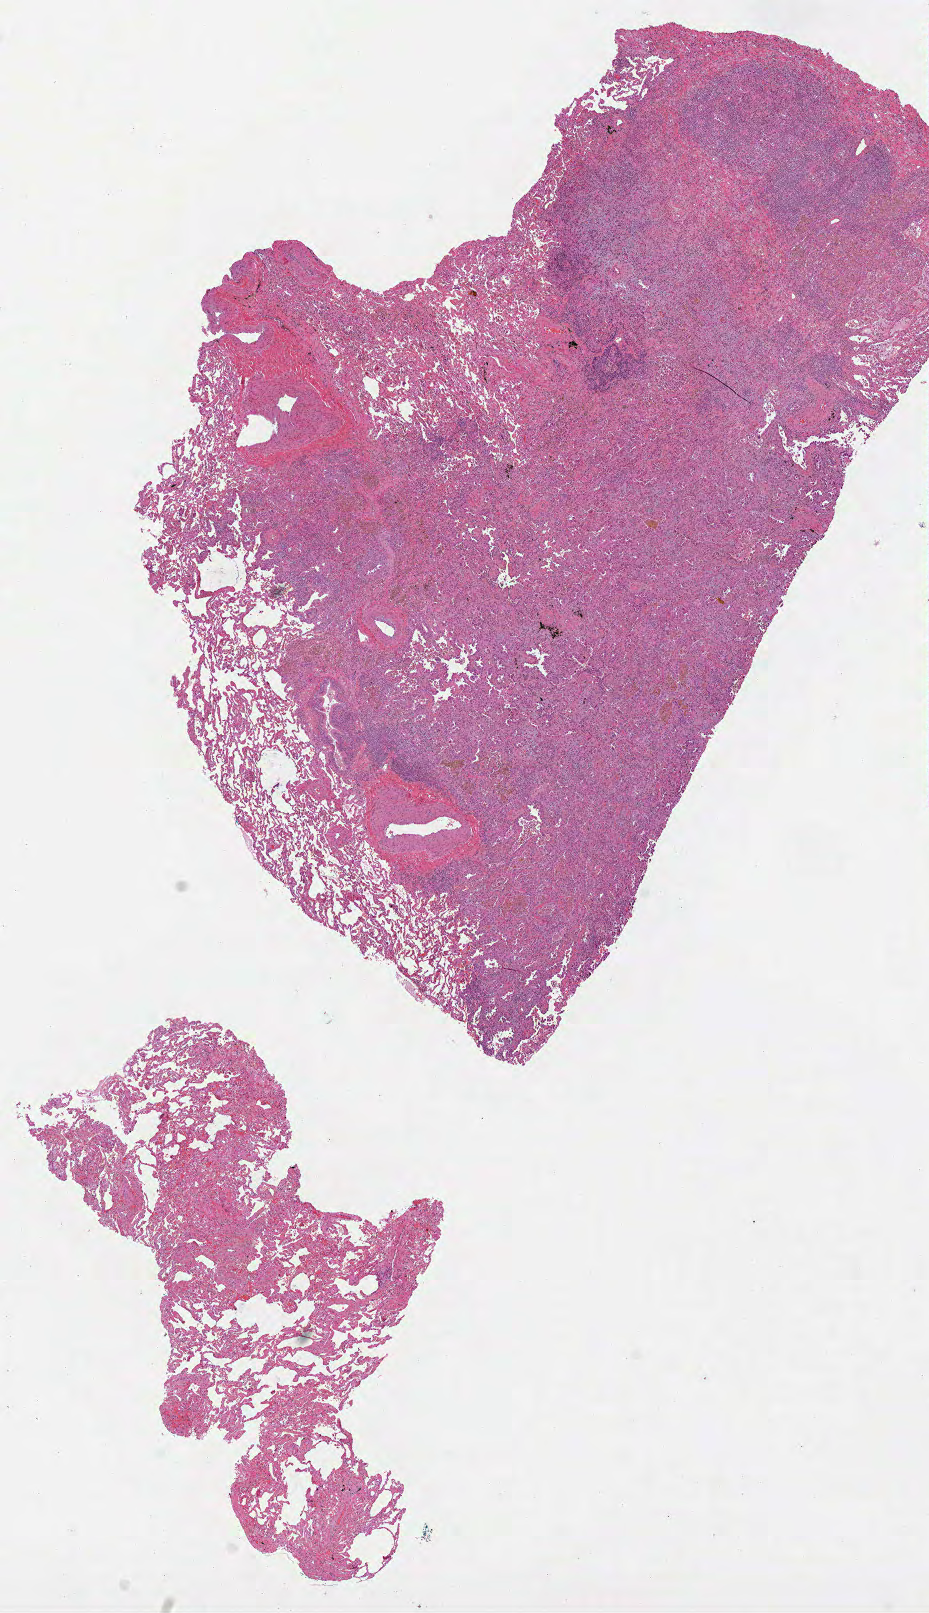
Whole-slide histology image, H&E-stained — a low-resolution overview of the entire scanned area, about 7.5 x 13.0 mm (from a 40x scan); FFPE section; lung, primary tumour sample. Female, age 55 years at initial diagnosis.
• laterality: right
• pathologic diagnosis: Adenocarcinoma, NOS (lower lobe, lung)
• AJCC pathologic stage: IB (7th edition)